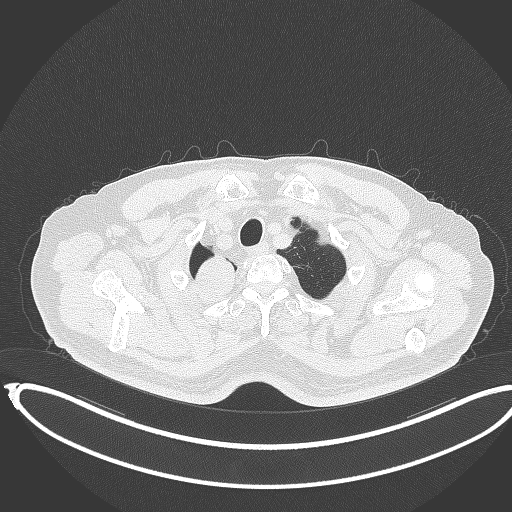
Chest CT, one axial slice. Position 338 of 403 along the scan axis. Reconstruction kernel B70f. 120 kVp. Lung window (W 1500 / L -600 HU). 512 × 512 image matrix. Male patient, age 68 years. Case-level facts recorded for this patient, not image findings: clinical TNM (as recorded): T2a N0 M0.
Outlined on this slice (rectangle marked by the reading radiologist):
- lung tumour (recorded histology: adenocarcinoma): bounding box [x1, y1, x2, y2] px = [183, 245, 239, 310]